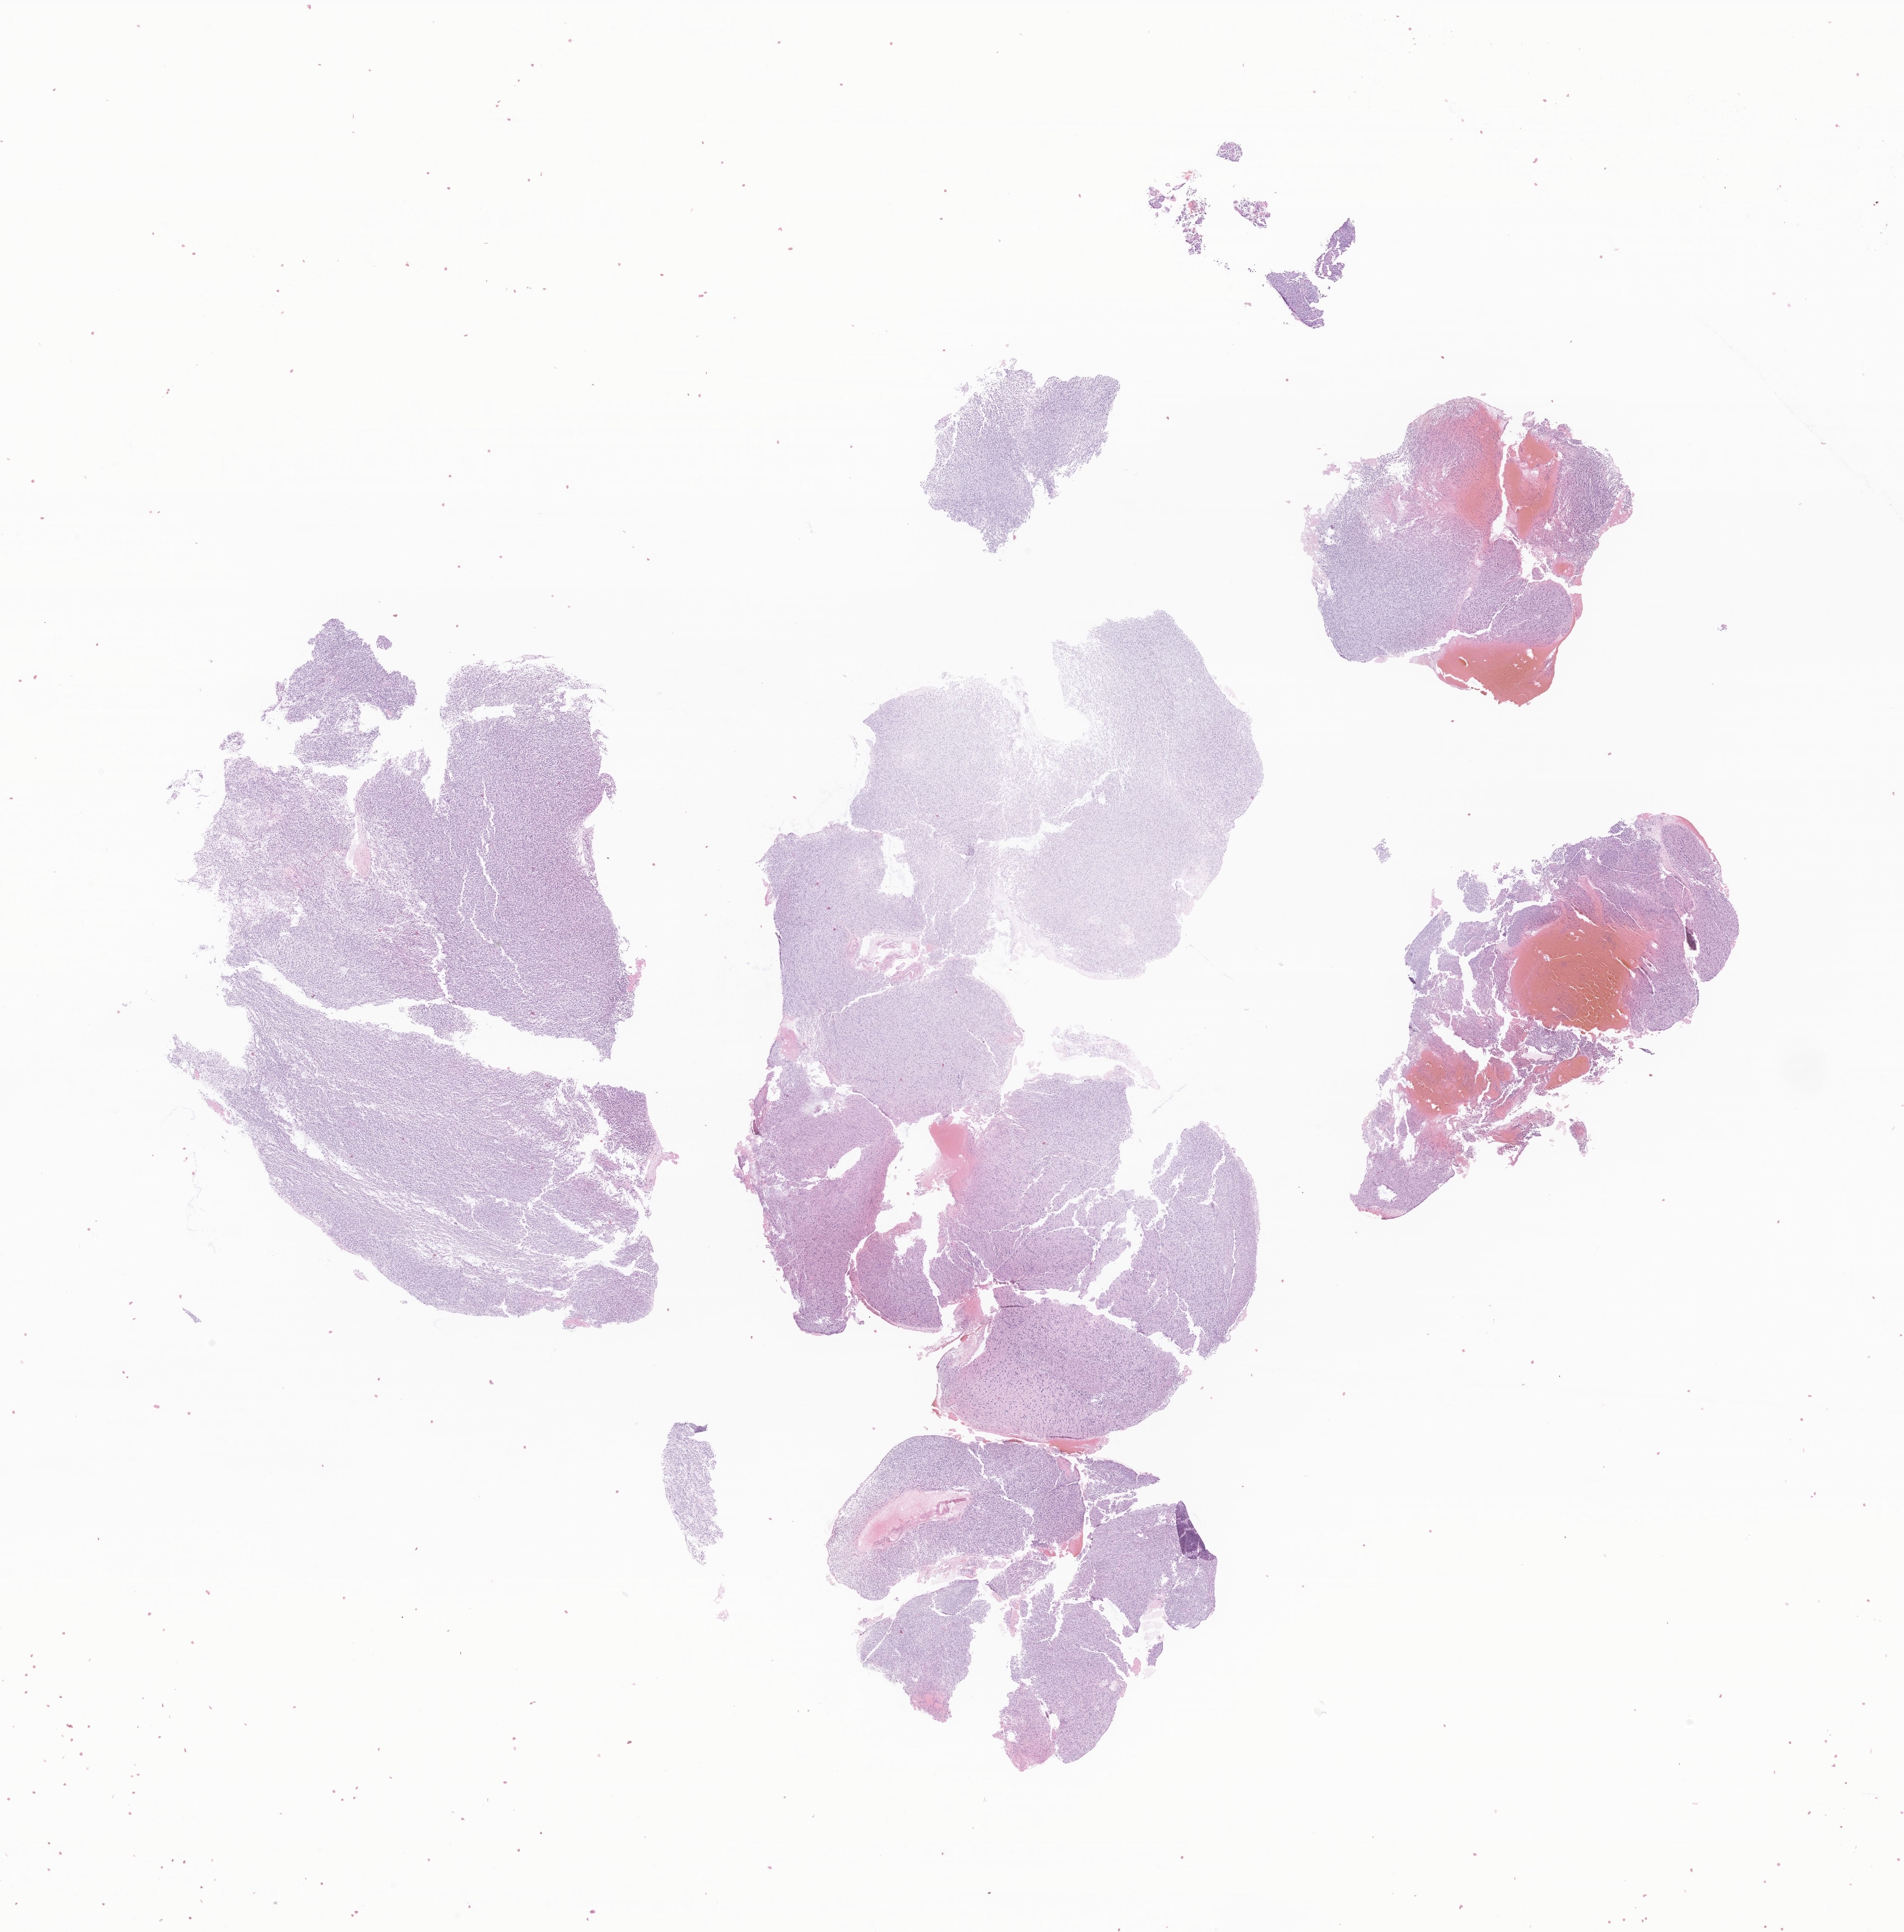
H&E whole-slide image of tumor tissue from the cerebrum, low-resolution overview of the scanned area, about 21.1 x 21.4 mm, formalin-fixed paraffin-embedded section. Patient: female, age 38 months (3 years 2 months).
Recorded diagnosis: Glioma, malignant.